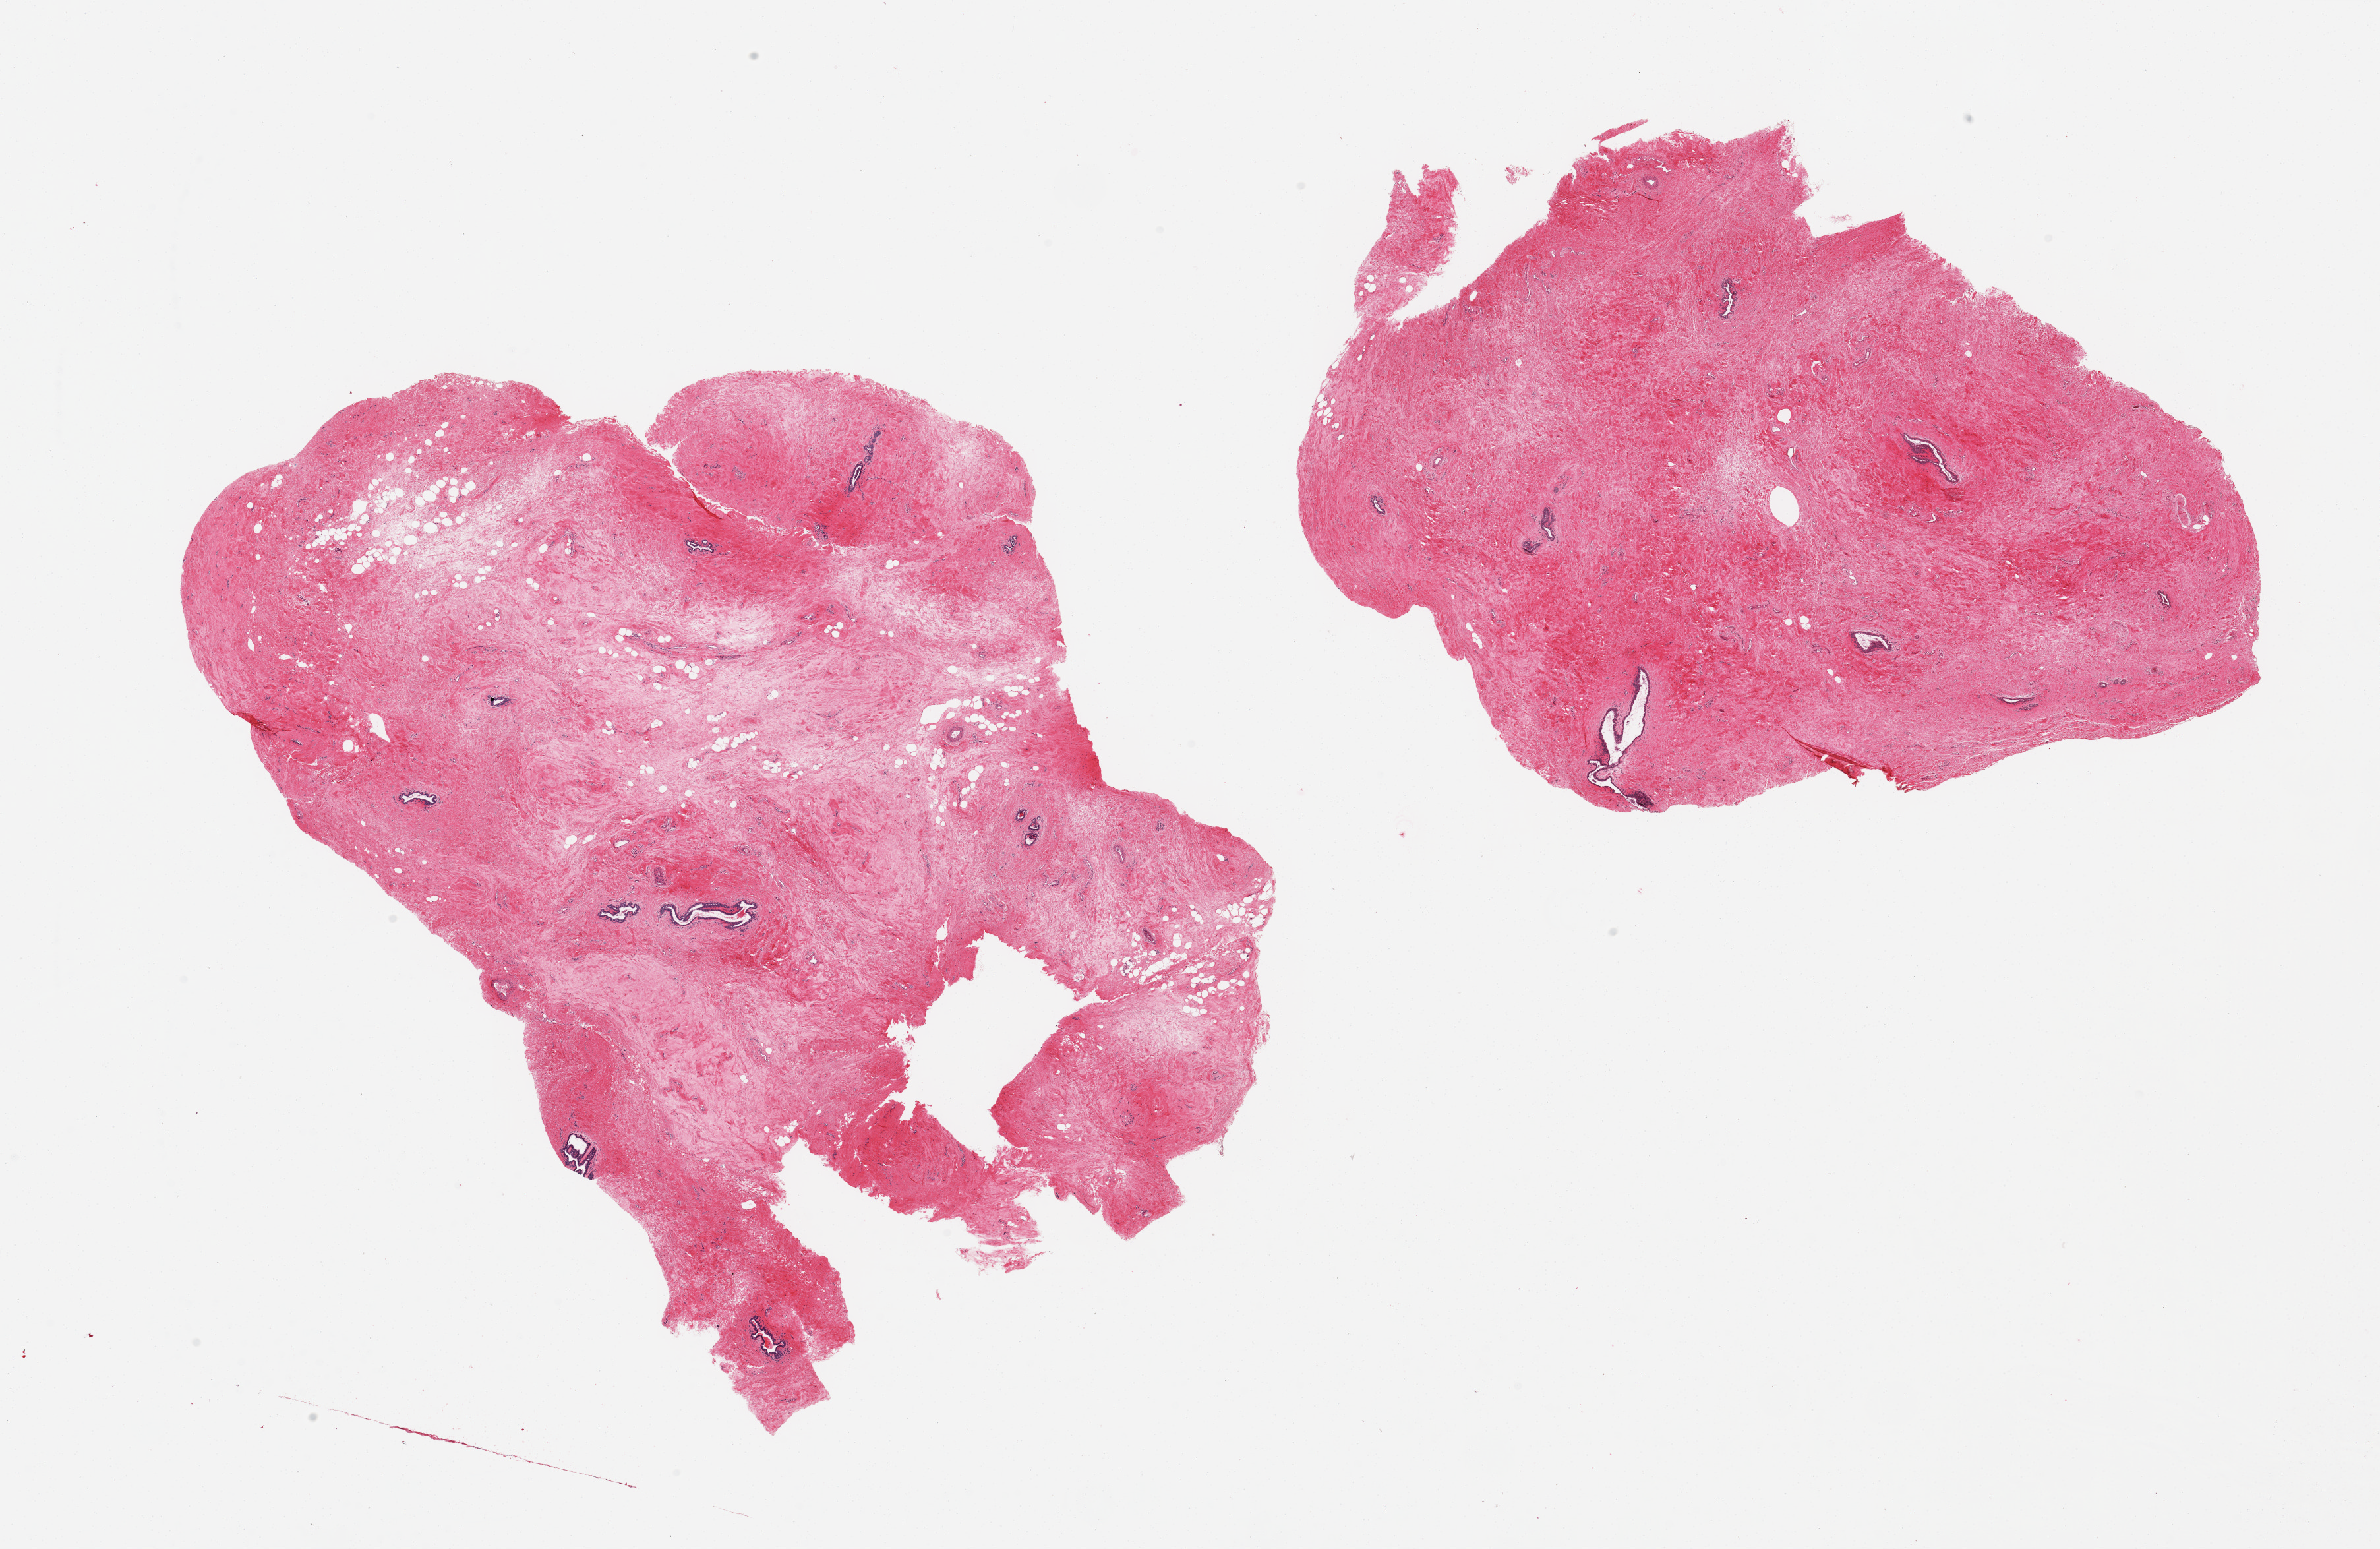
H&E whole-slide image, brightfield, low-resolution overview of the scanned area, about 28.5 x 18.6 mm. PAXgene-fixed paraffin-embedded (PFPE) section. Target tissue: breast. Tissue donor sample. Donor: male.
Pathologist's review note for this sample: 2 pieces; gynecomastoid hyperplasia.